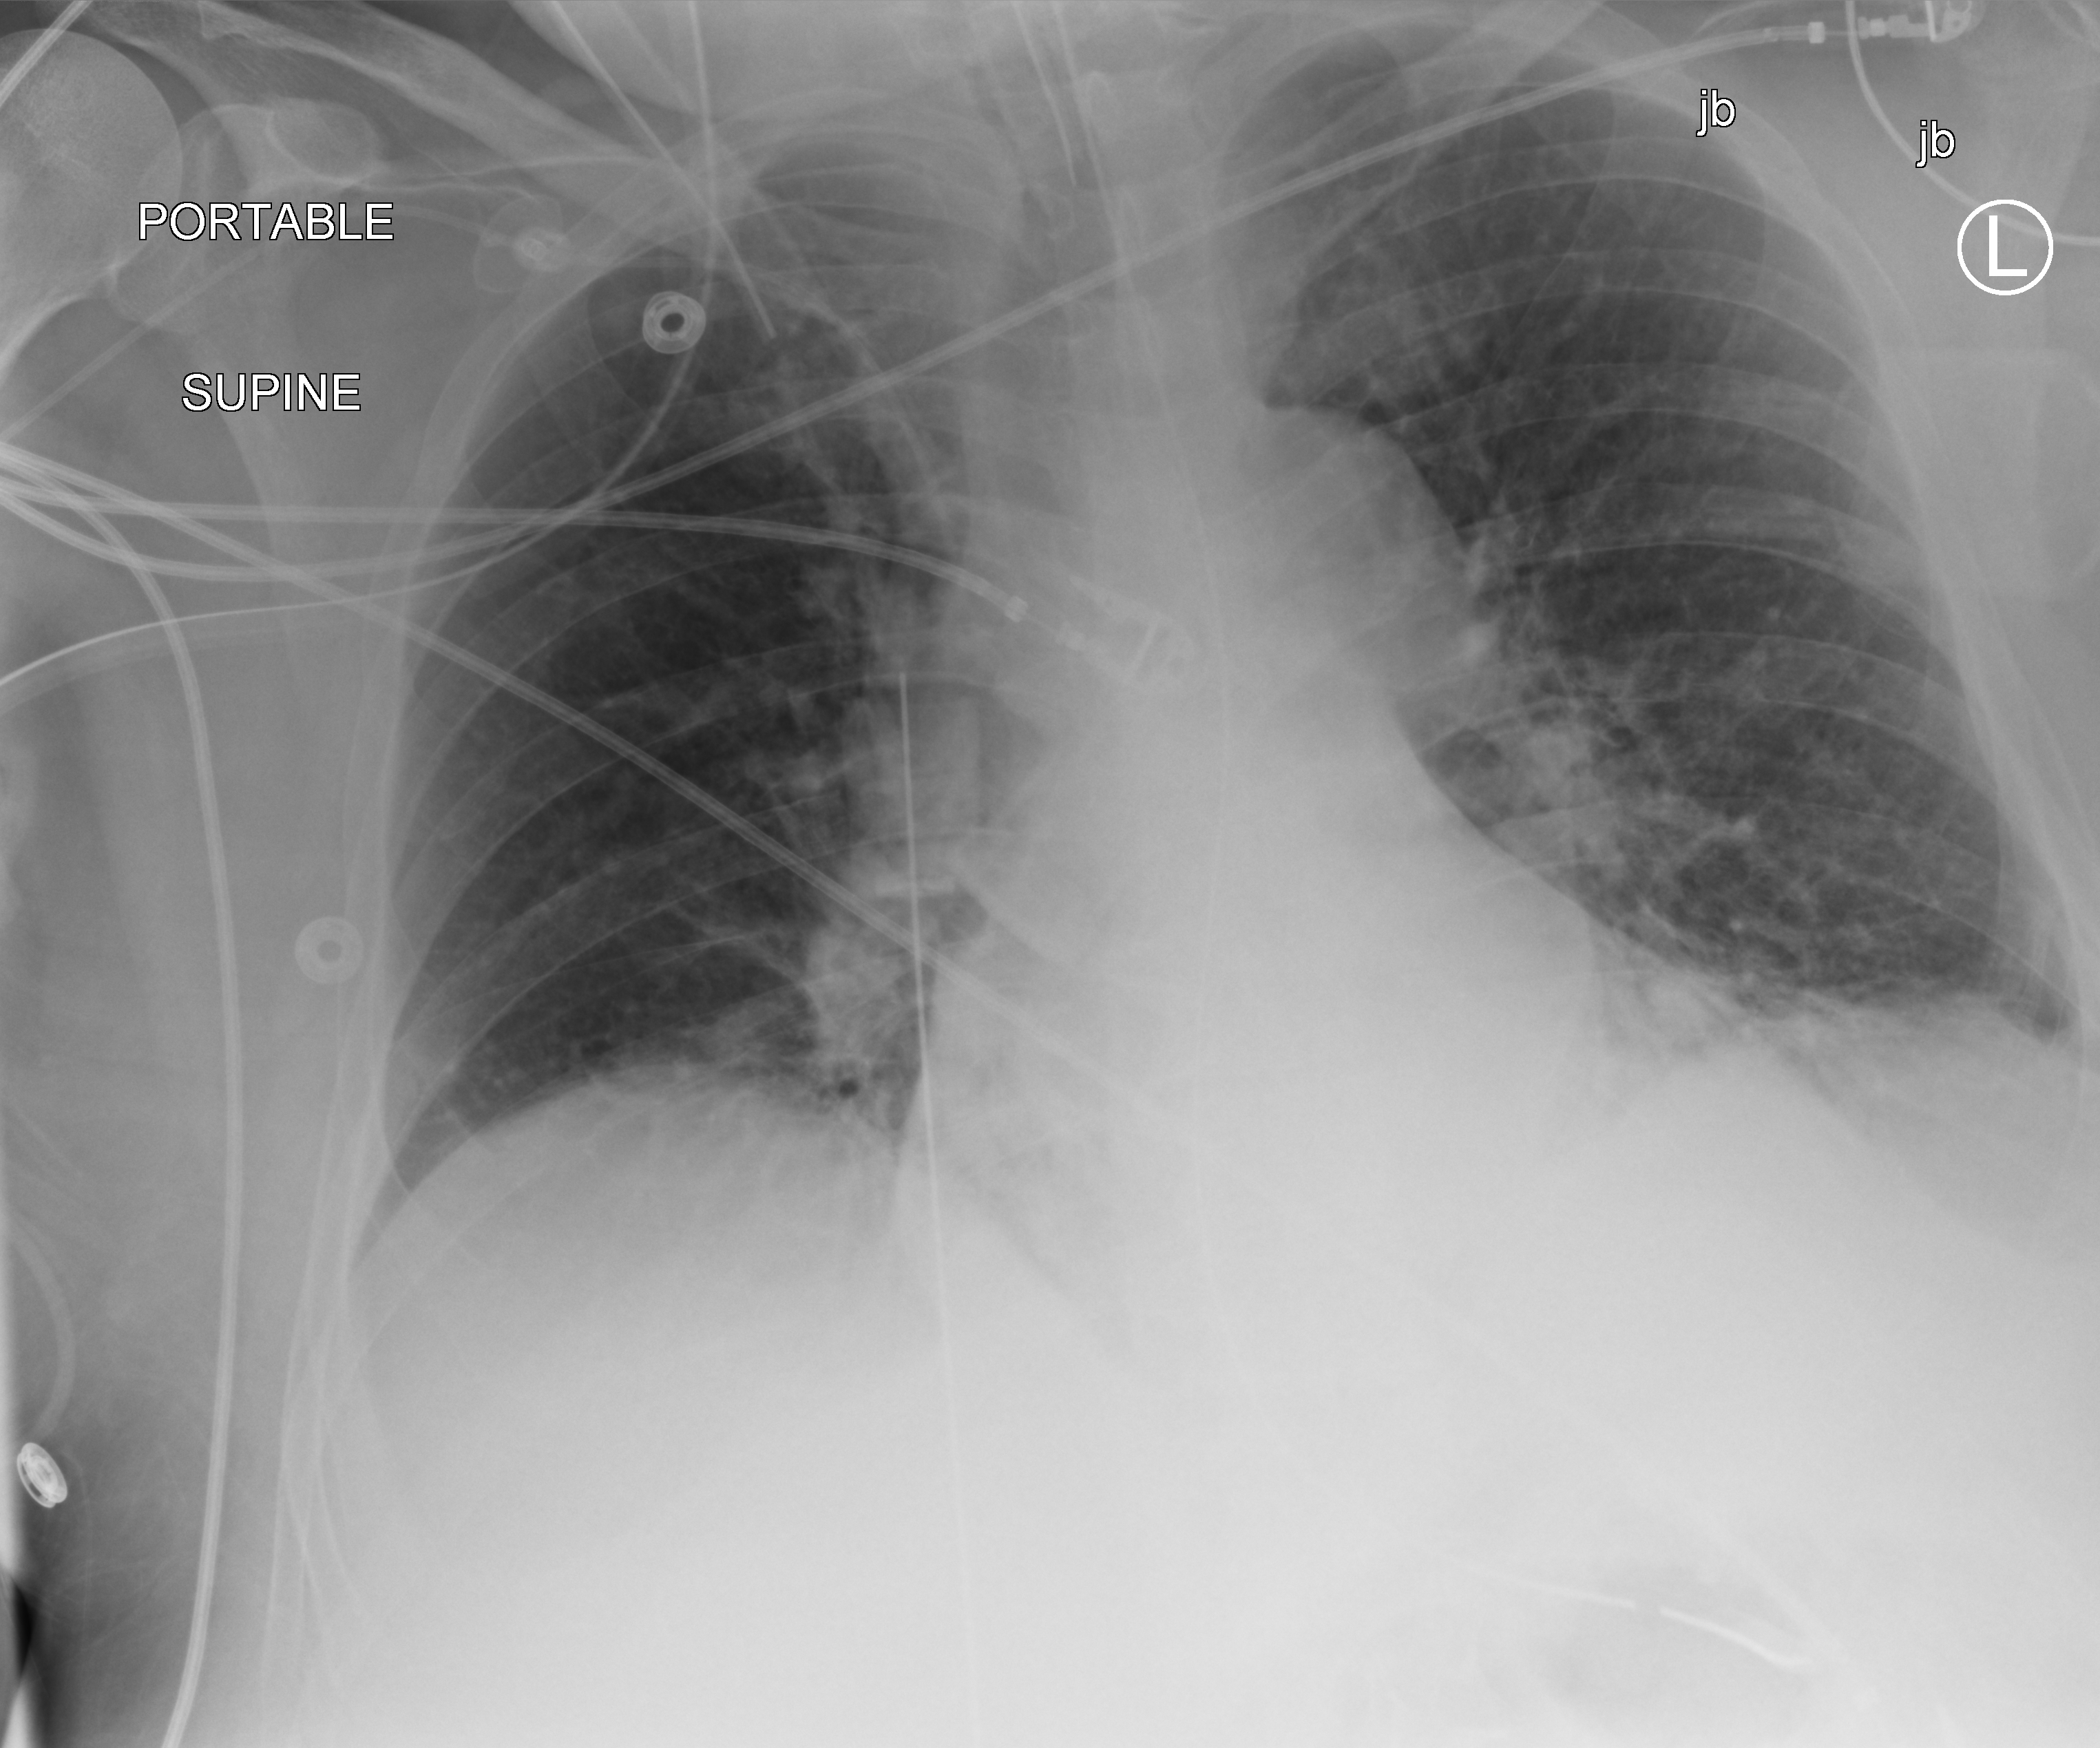
Bedside chest radiograph (computed radiography). Patient hospitalised with COVID-19; male, aged 60–74 years.
From the hospital-stay record, not from the radiograph (when in the stay this image was taken is not recorded): chronic kidney disease (admission record): no; length of hospital stay: 22 days.